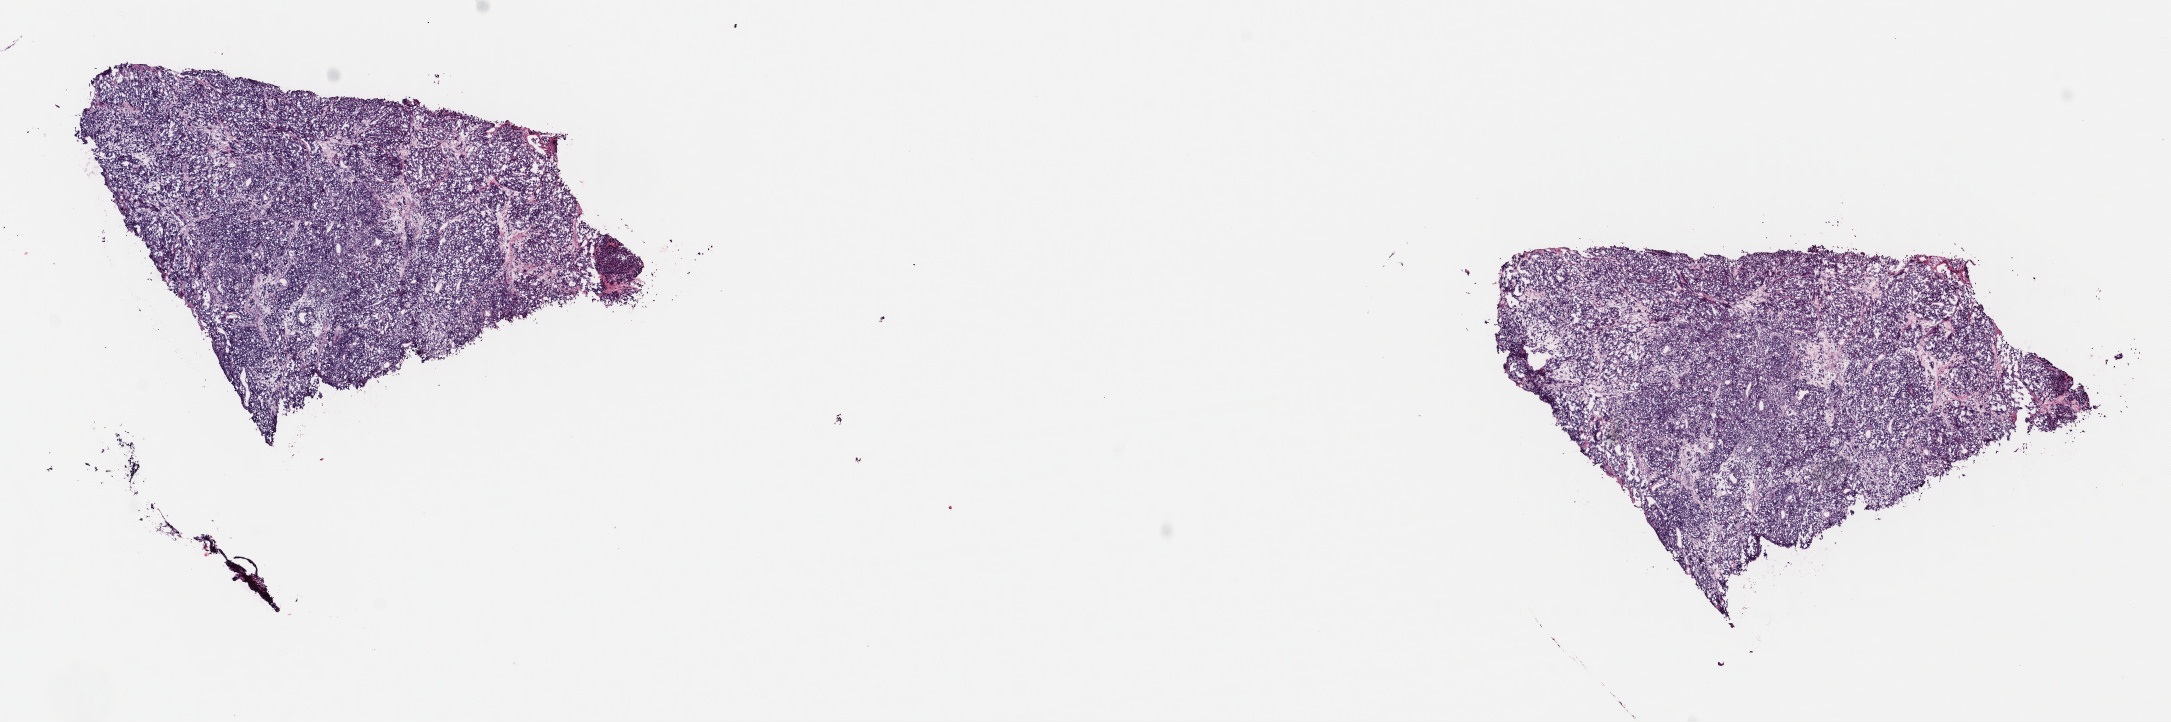
H&E whole-slide image, shown as a low-resolution overview of the whole scanned area (about 17.1 x 5.7 mm); frozen section from the top of the tissue portion; metastatic tumour sample. Patient: female, age at initial diagnosis 63 years.
This section: metastatic tumour tissue. Patient diagnosis: Malignant melanoma, NOS.